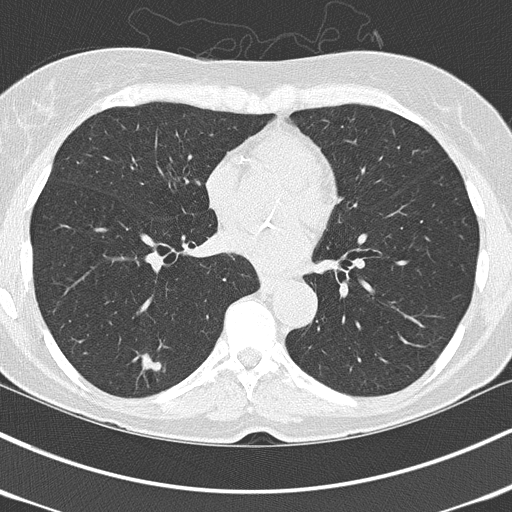
Axial slice from a low-dose chest CT screening exam, third annual screen, lung window (W 1500 / L -600 HU), 2 mm slice thickness, lung (sharp) reconstruction kernel (B50f), 512 × 512 image matrix, field of view 318 × 318 mm. Female participant, aged 67 years at enrolment. Current smoker at enrolment.
Expert reader's lesion annotation, bounding box <129,347,168,382> (left, top, right, bottom; pixels). The screening reader recorded 3 non-calcified nodules or masses ≥4 mm on this exam; which of them this box marks is not recorded. Lung cancer was diagnosed 64 days after this screen: adenocarcinoma, NOS, left lower lobe, poorly differentiated (G3), stage IA (AJCC 6th edition), 25 mm at pathology.